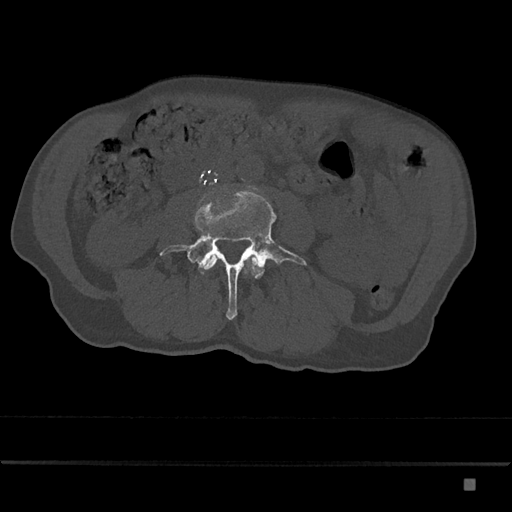
CT including the spine, one axial slice; slice 353 of 797 in the series (ordered by position); bone window (W 1800 / L 400 HU); 0.5 mm slice thickness; 512 × 512 image matrix, field of view 390 × 390 mm. Patient: male, 72 years. From the clinical record (not read from this slice): primary cancer: prostate.
Annotated regions visible in this slice (semi-automatic segmentation, software-assisted and operator-edited):
- L3 vertebra: bounding box <204,255,258,270> (left, top, right, bottom; pixels)
- L4 vertebra: <160,189,307,320>